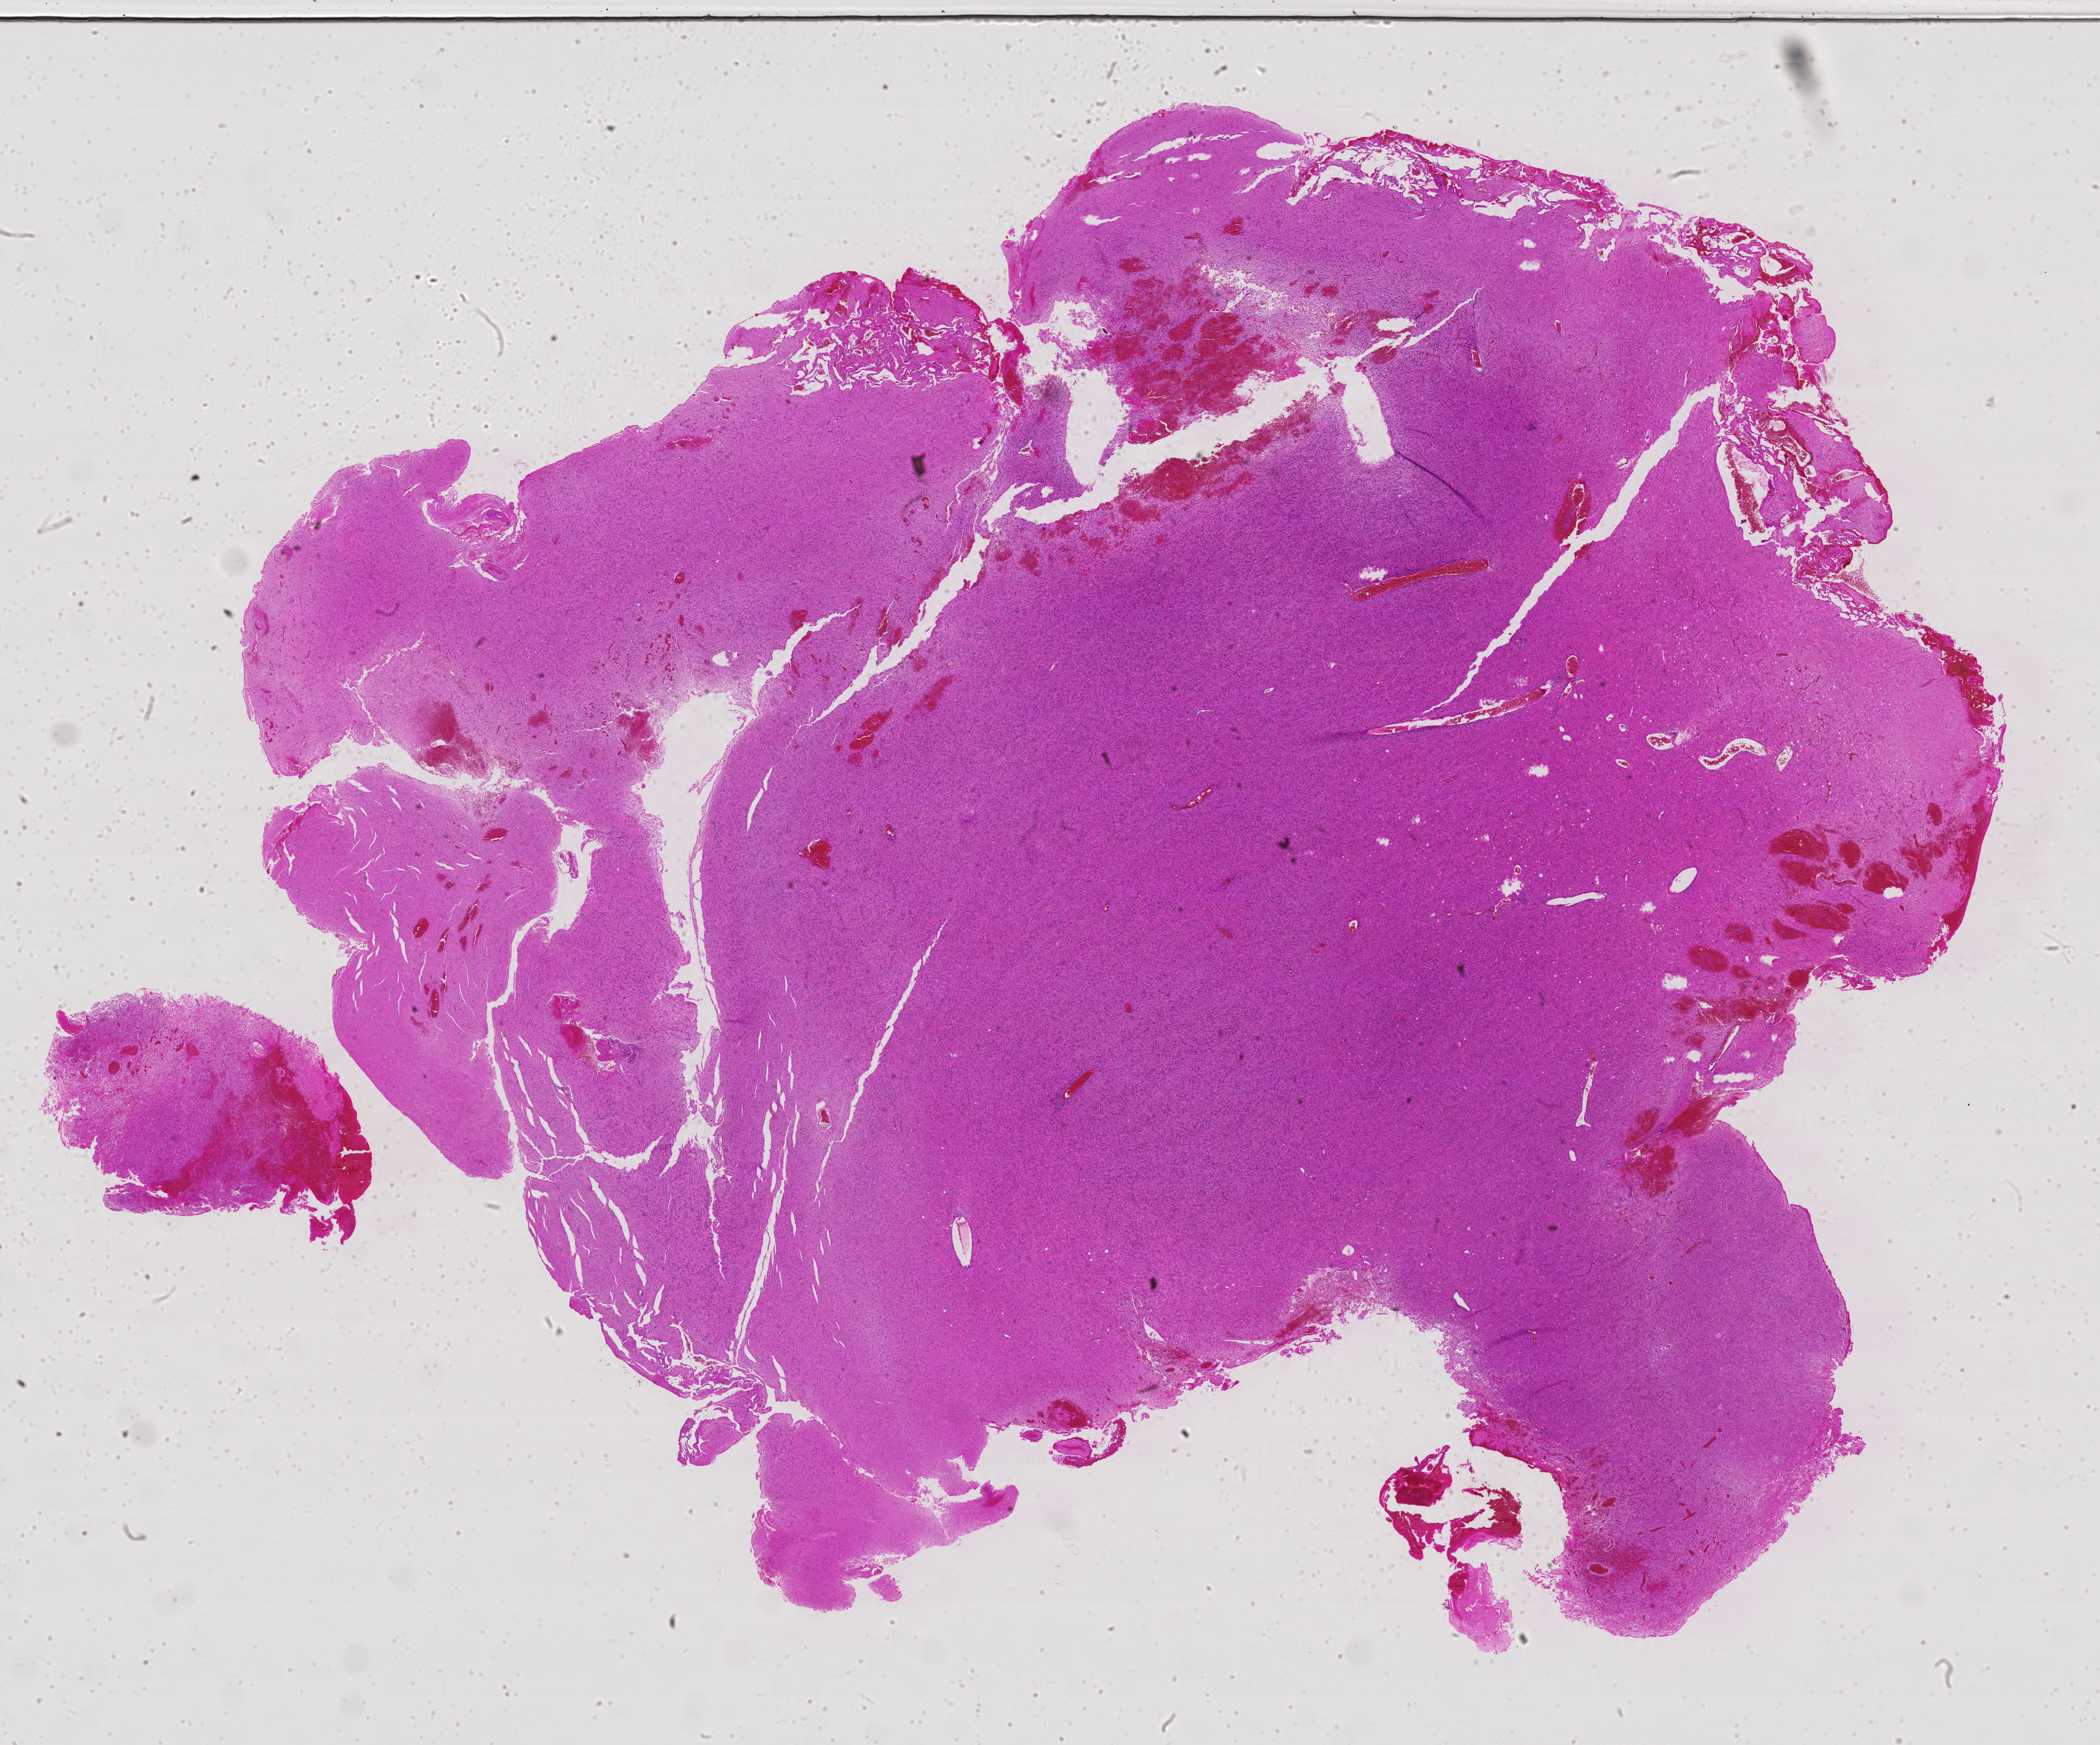
Whole-slide histology image, H&E, low-resolution overview of the scanned area, about 28.3 x 23.5 mm. Formalin-fixed paraffin-embedded (FFPE) diagnostic section. Primary tumour sample from the brain. Patient: male, age at initial diagnosis 55 years.
Histologic diagnosis: Astrocytoma, anaplastic.